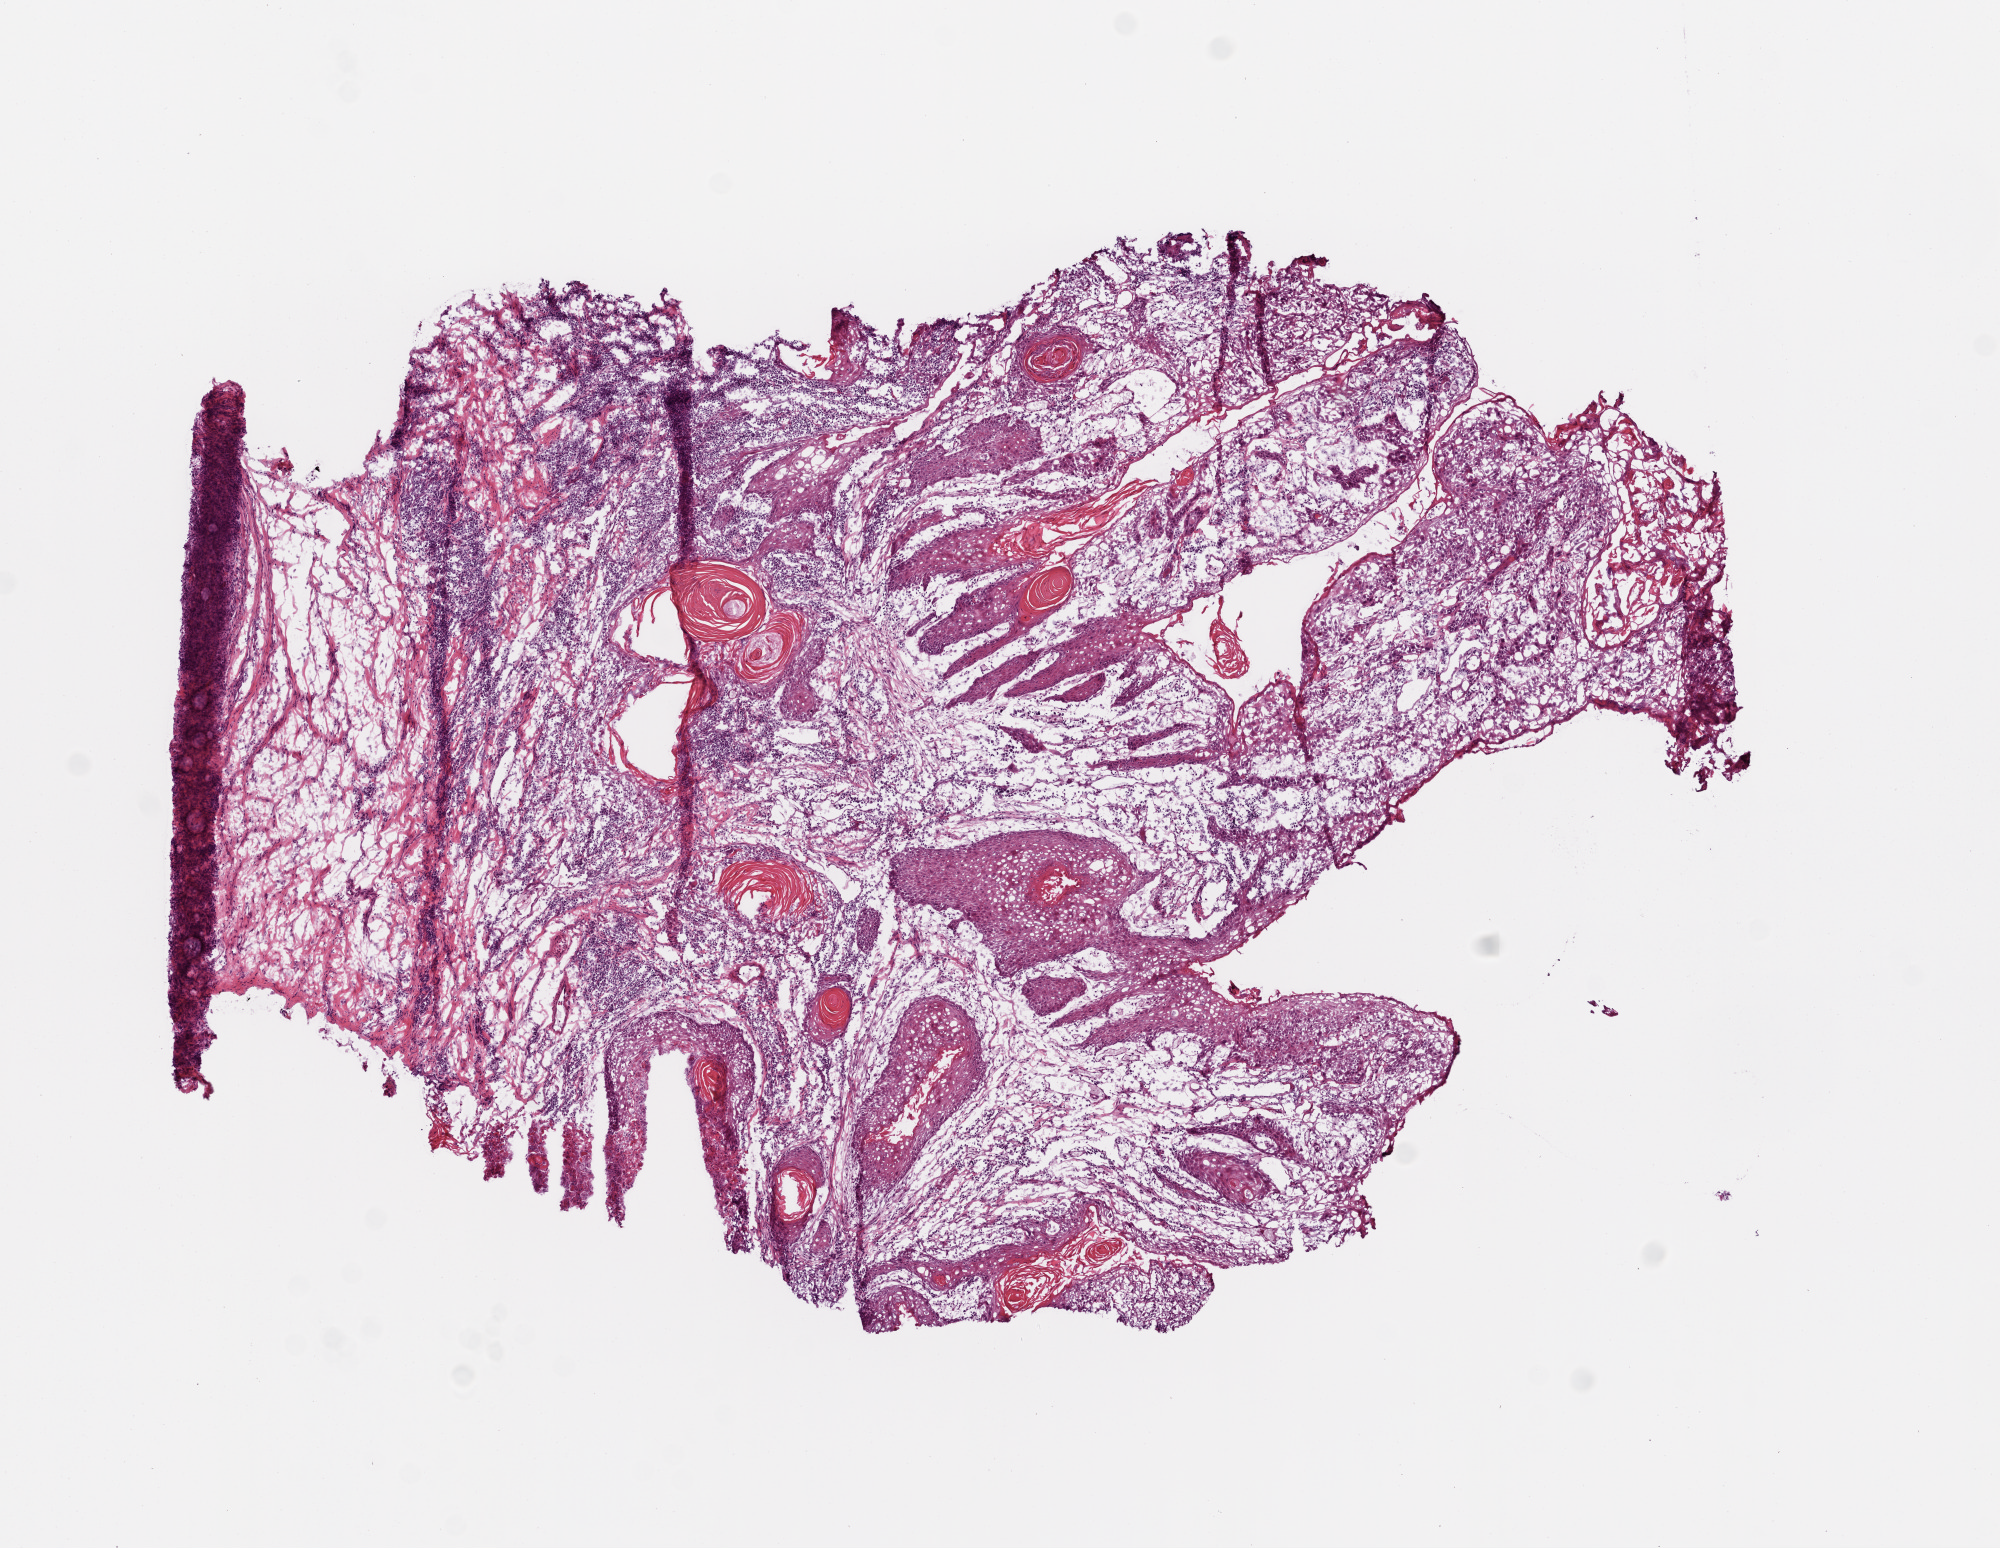
H&E-stained whole-slide image, a low-resolution overview of the entire scanned area, about 8.0 x 6.2 mm (from a 20x scan); frozen section from the top of the tissue portion; sample: primary tumour, head and neck. Male, age 60 years at initial diagnosis.
Histologic diagnosis: Squamous cell carcinoma, NOS (floor of mouth, NOS).